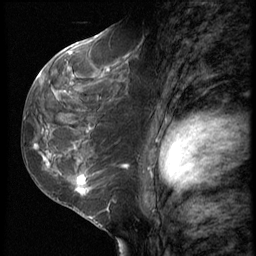
Breast MRI (dynamic contrast-enhanced), one sagittal slice; slice 34 of 62 in the series (ordered by position); 3 images stored at this slice position (order not interpretable as contrast timing); 1.5 T; TE 4.2 ms, TR 9 ms; 2.5 mm slice thickness; 256 × 256 image matrix, field of view 180 × 180 mm. Patient: female, 50 years. Case-level facts recorded for this patient, not image findings: setting: breast cancer imaged before/during neoadjuvant chemotherapy; receptor status: HR-positive, HER2-negative.
Outlined on this slice (semi-automatic segmentation, software-assisted and operator-edited):
- analysis volume of interest (the breast-tissue region the enhancement analysis was run in; not a lesion): bounding box [x1, y1, x2, y2] px = [32, 91, 118, 209]
- tumour enhancement mask (voxels above the 140 % enhancement threshold inside the analysis volume of interest): [35, 144, 92, 194]